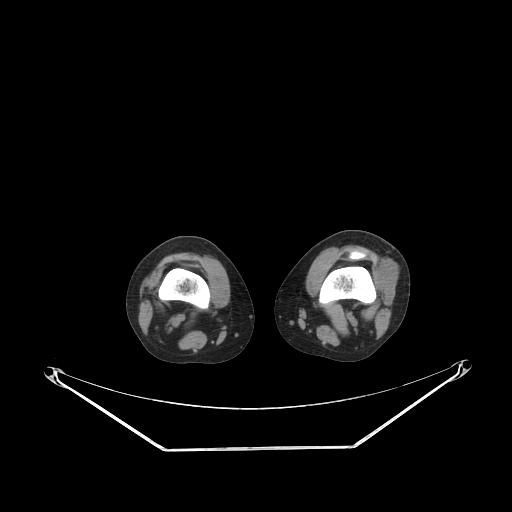
CT of an extremity soft-tissue mass (from a PET/CT study), one axial slice. Position 169 of 223 along the scan axis. Reconstruction kernel STANDARD. 140 kVp. Soft-tissue window (W 400 / L 40 HU). 3.75 mm slice thickness. 512 × 512 image matrix, field of view 500 × 500 mm. Female patient. Case-level facts recorded for this patient, not image findings: histological type: spindle cell suggestive of biphasic synovial sarcoma; grade: intermediate; site of the primary tumour: left knee.
Annotated regions visible in this slice (expert contour drawn on MRI and transferred to this co-registered scan by the dataset authors):
- gross tumour volume including surrounding oedema: bounding box <374,262,396,305> (left, top, right, bottom; pixels)
- gross tumour volume (mass): <374,267,396,305>